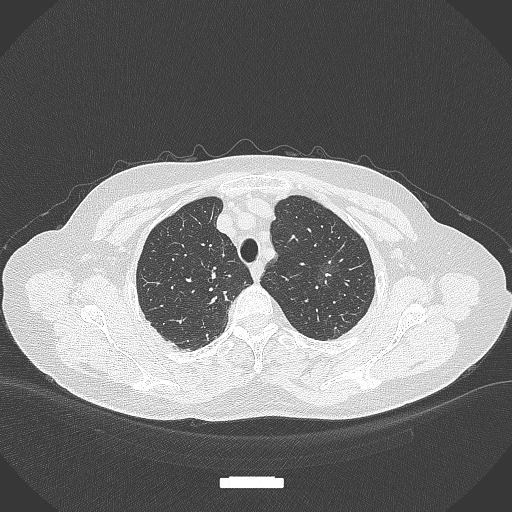
Chest CT, one axial slice; slice 296 of 369 in the series (ordered by position); 120 kVp; lung window (W 1500 / L -600 HU); 512 × 512 image matrix. Female patient, age 64 years. Case-level facts recorded for this patient, not image findings: clinical TNM (as recorded): T1c N0 M0.
Outlined on this slice (bounding box drawn by a radiologist):
- lung tumour (recorded histology: adenocarcinoma): bounding box (x1, y1, x2, y2) in pixels: (312, 251, 346, 290)